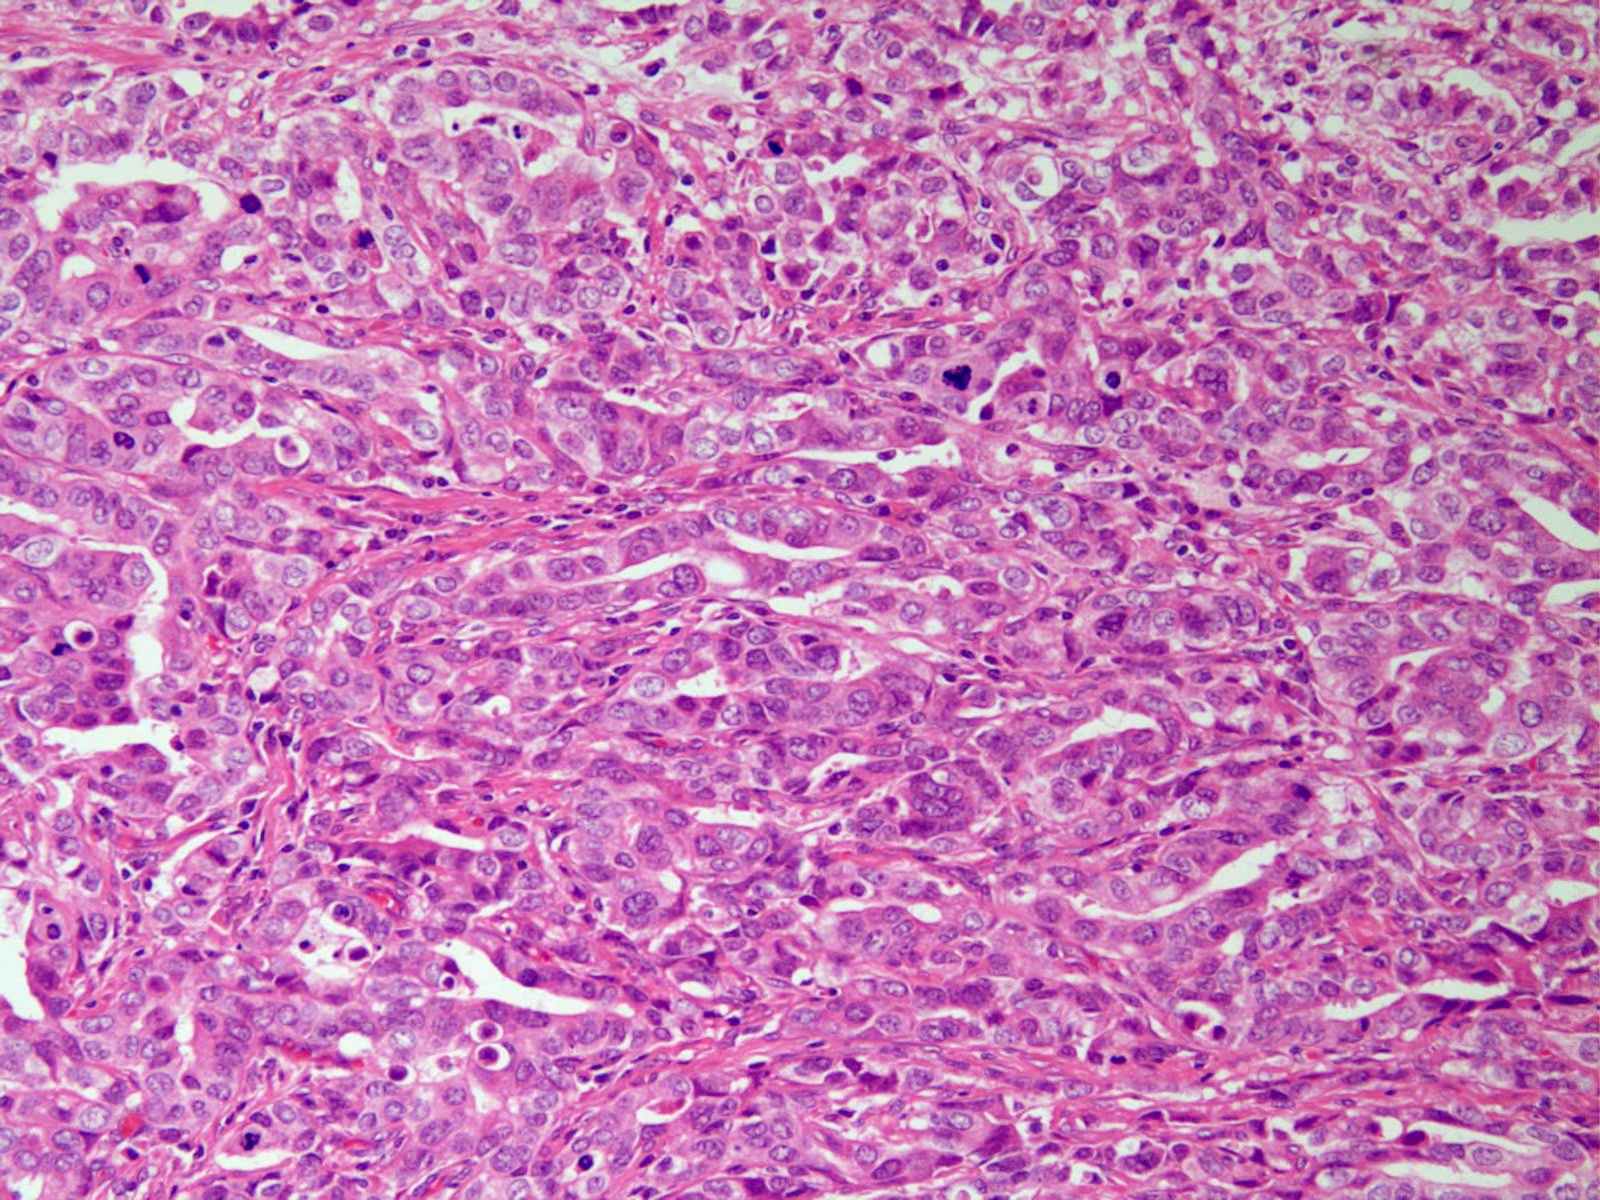
H&E-stained micrograph of a single small tissue field — about 0.8 x 0.6 mm across; formalin-fixed paraffin-embedded (FFPE) diagnostic section; primary tumour sample from the stomach. Female patient; age at initial diagnosis 55 years. Histologic grade: G3 (poorly differentiated).
Diagnosis: Adenocarcinoma, NOS. AJCC pathologic stage: IIIA (6th edition). TNM: T3 N1 M0.